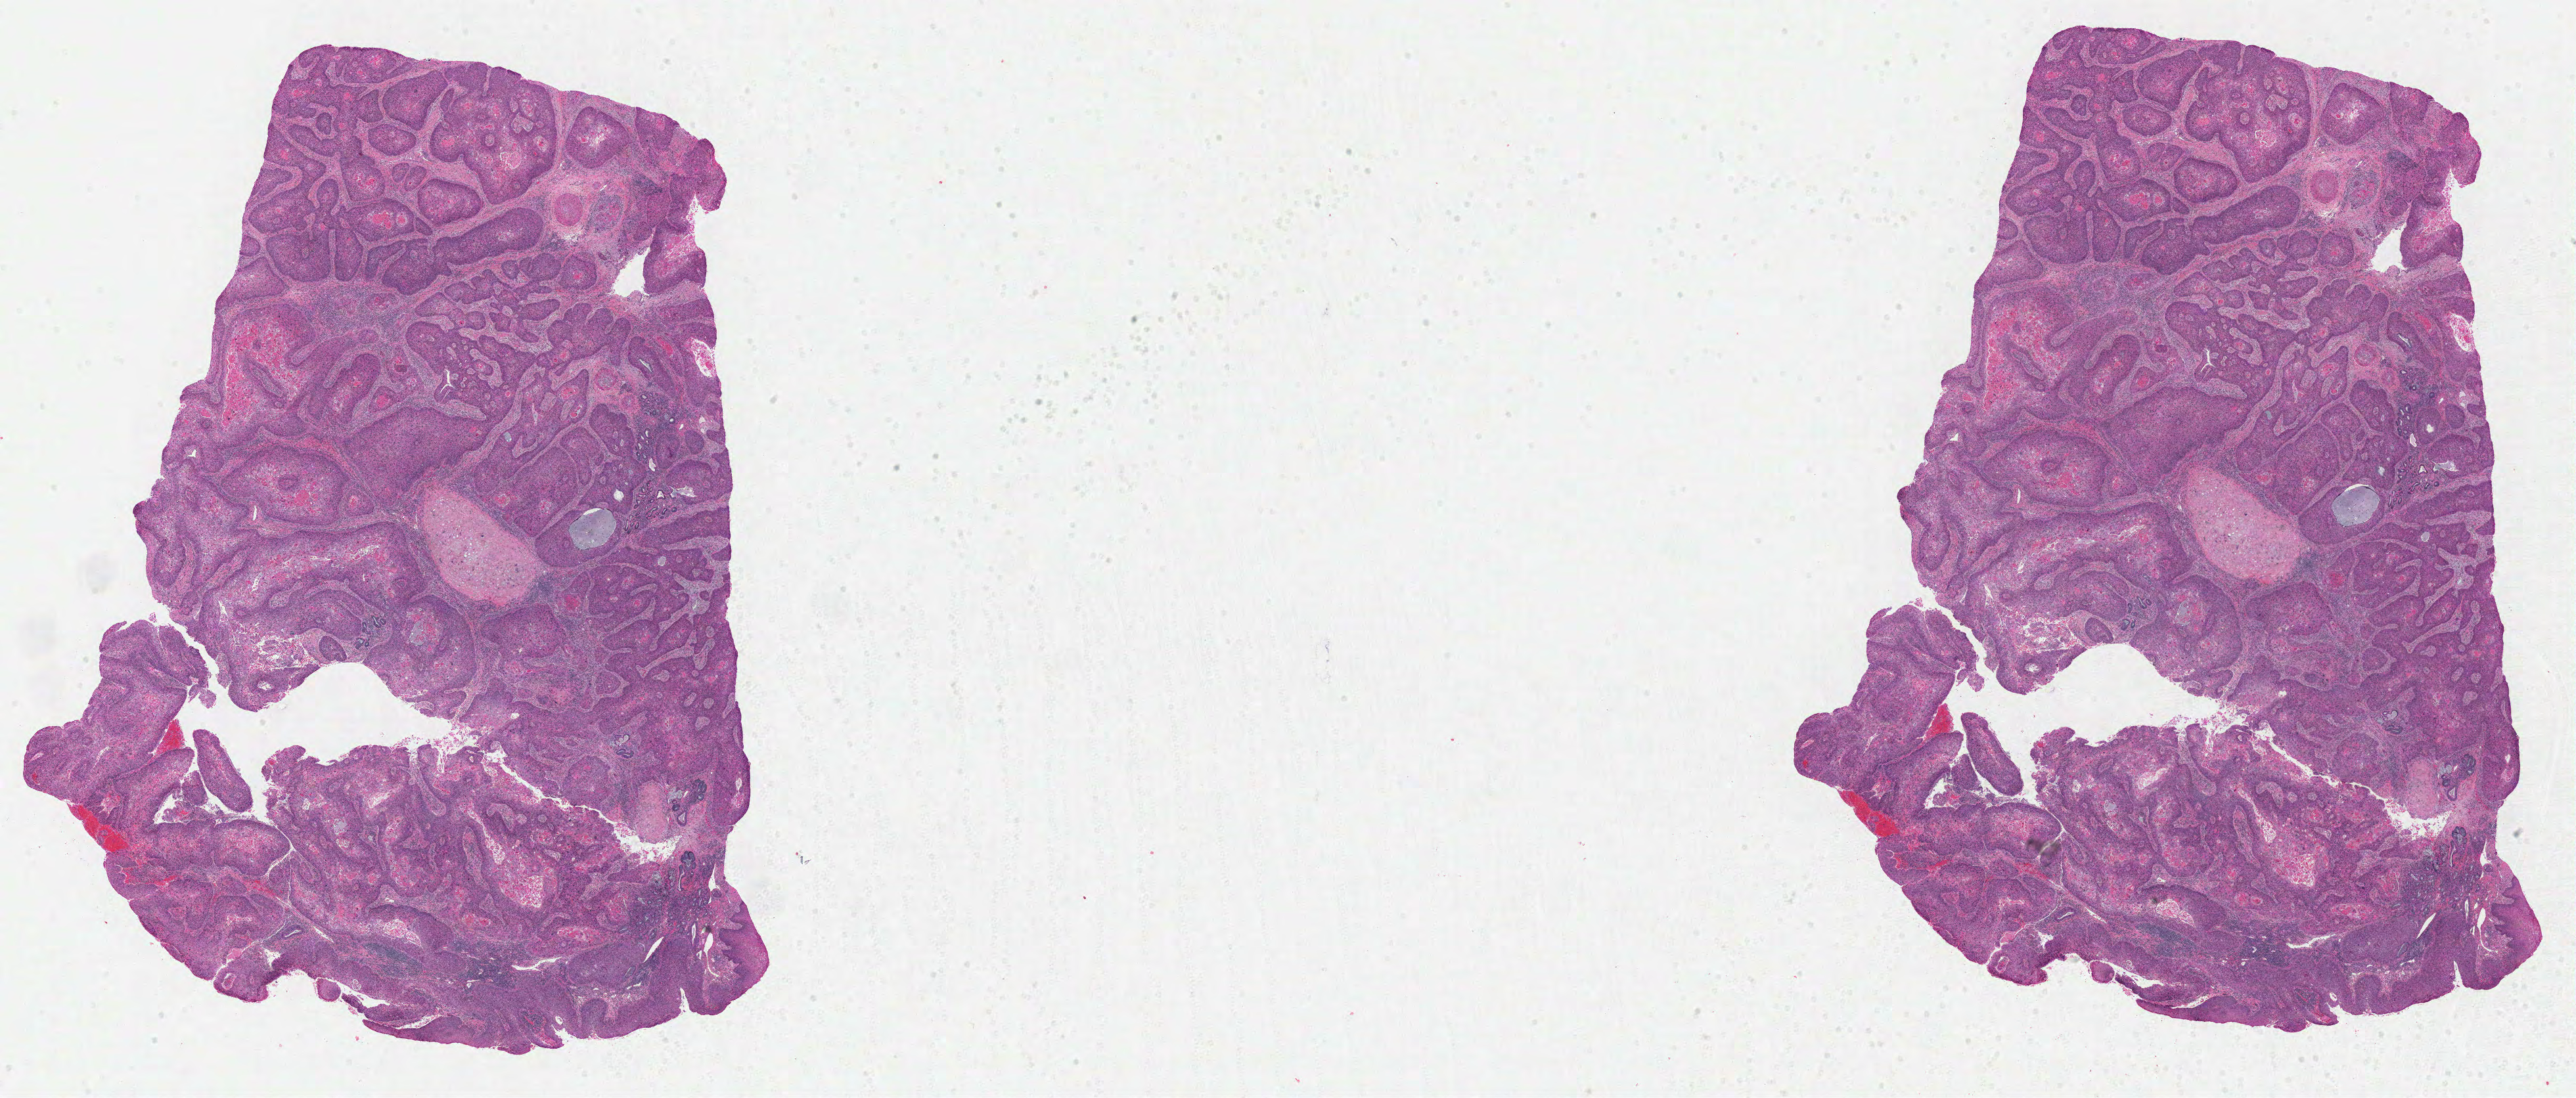
Digitized H&E-stained tissue section (whole slide) — whole scanned area (about 30.8 x 13.1 mm) shown as a low-resolution overview. FFPE section. Primary tumour sample from the head and neck. Male patient; age at initial diagnosis 54 years. Histologic grade: G2 (moderately differentiated).
• AJCC pathologic stage: IVA (7th edition)
• histologic diagnosis: Squamous cell carcinoma, NOS (larynx, NOS)
• laterality: right
• lymph nodes positive (case pathology): 1 of 68 examined